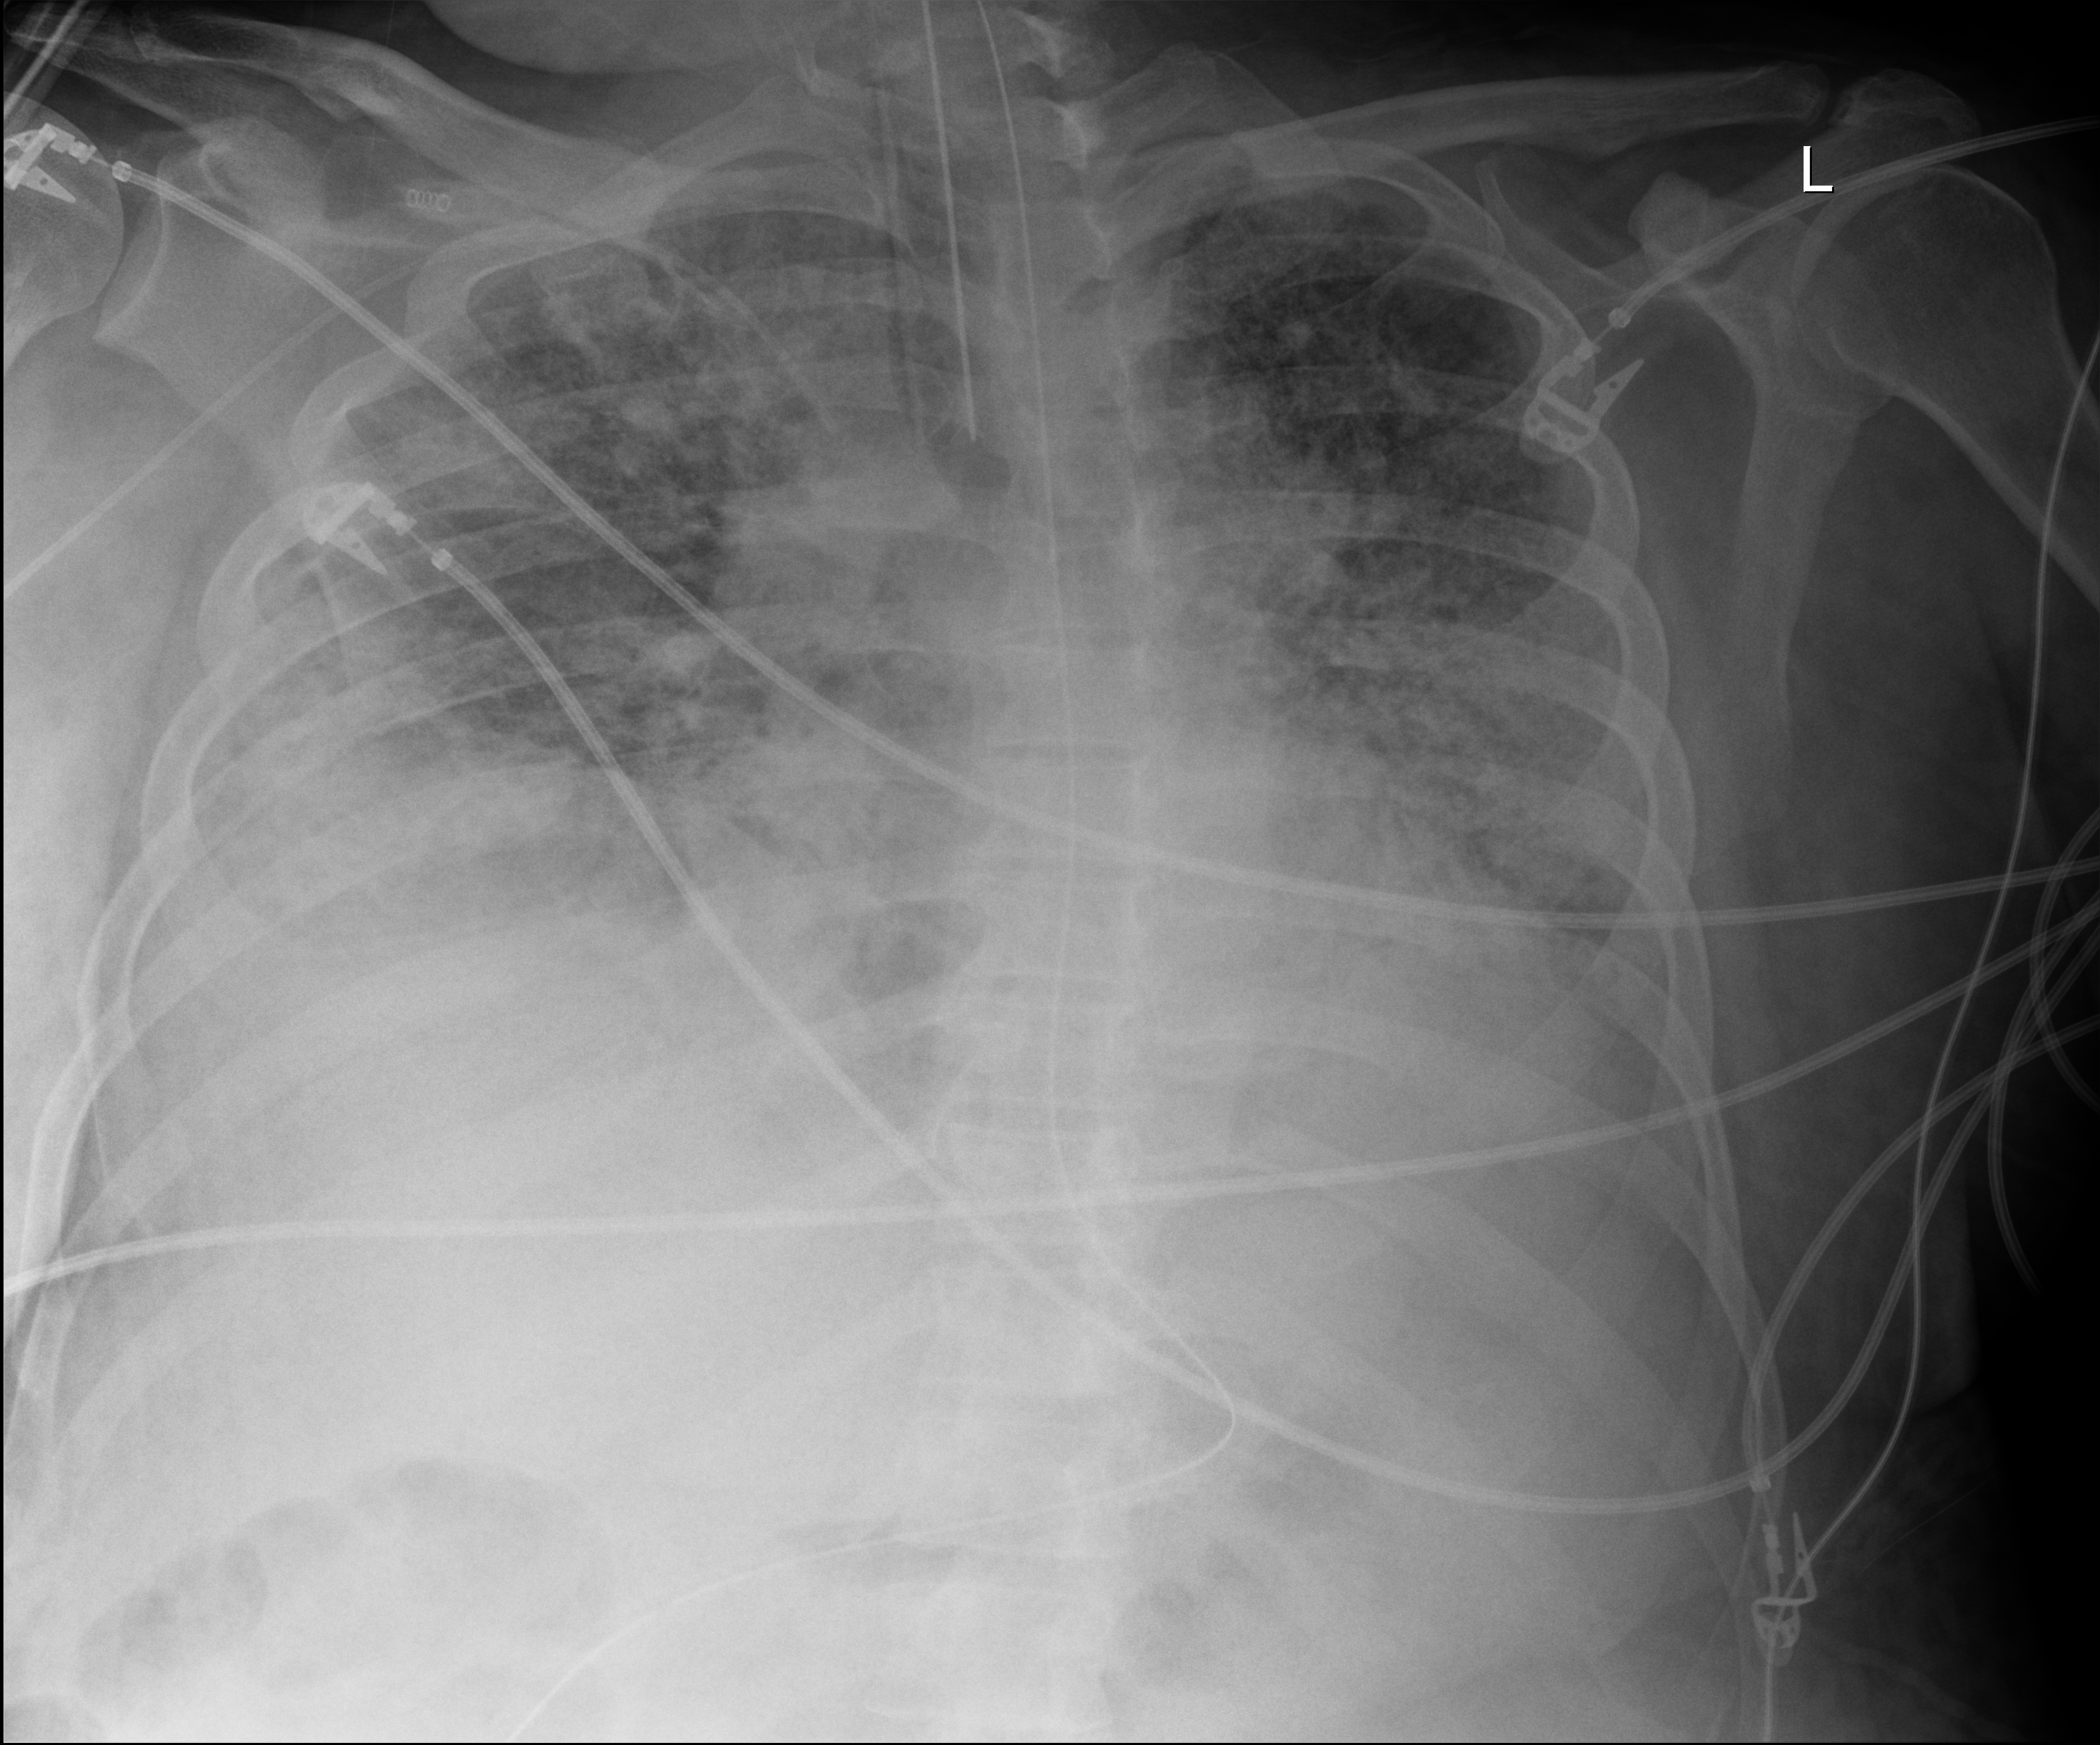
Chest X-ray (portable). Patient hospitalised with COVID-19; male, aged 18–59 years.
From the hospital-stay record, not from the radiograph (when in the stay this image was taken is not recorded): length of hospital stay: 96 days; mechanically ventilated during this hospital stay: yes; admitted to intensive care during this hospital stay: yes.